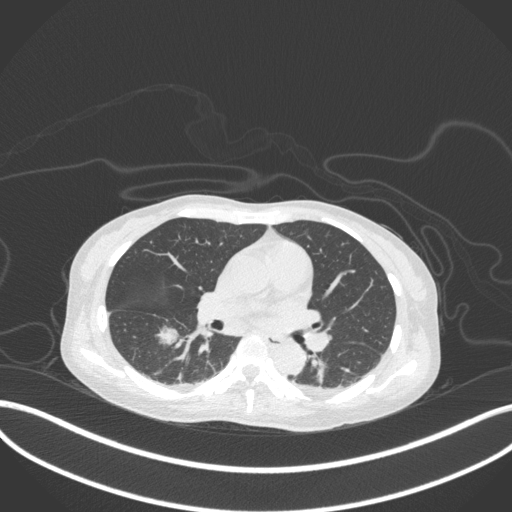
Chest CT, one axial slice; position 165 of 260 along the scan axis; 120 kVp; lung window (W 1500 / L -600 HU); 1 mm slice thickness; 512 × 512 image matrix, field of view 400 × 400 mm. Patient: female, 44 years. From the clinical record (not read from this slice): clinical TNM (as recorded): T1c N0 M0.
Annotated regions visible in this slice (rectangle marked by the reading radiologist):
- lung tumour (recorded histology: adenocarcinoma): bounding box [x1, y1, x2, y2] px = [152, 324, 181, 348]